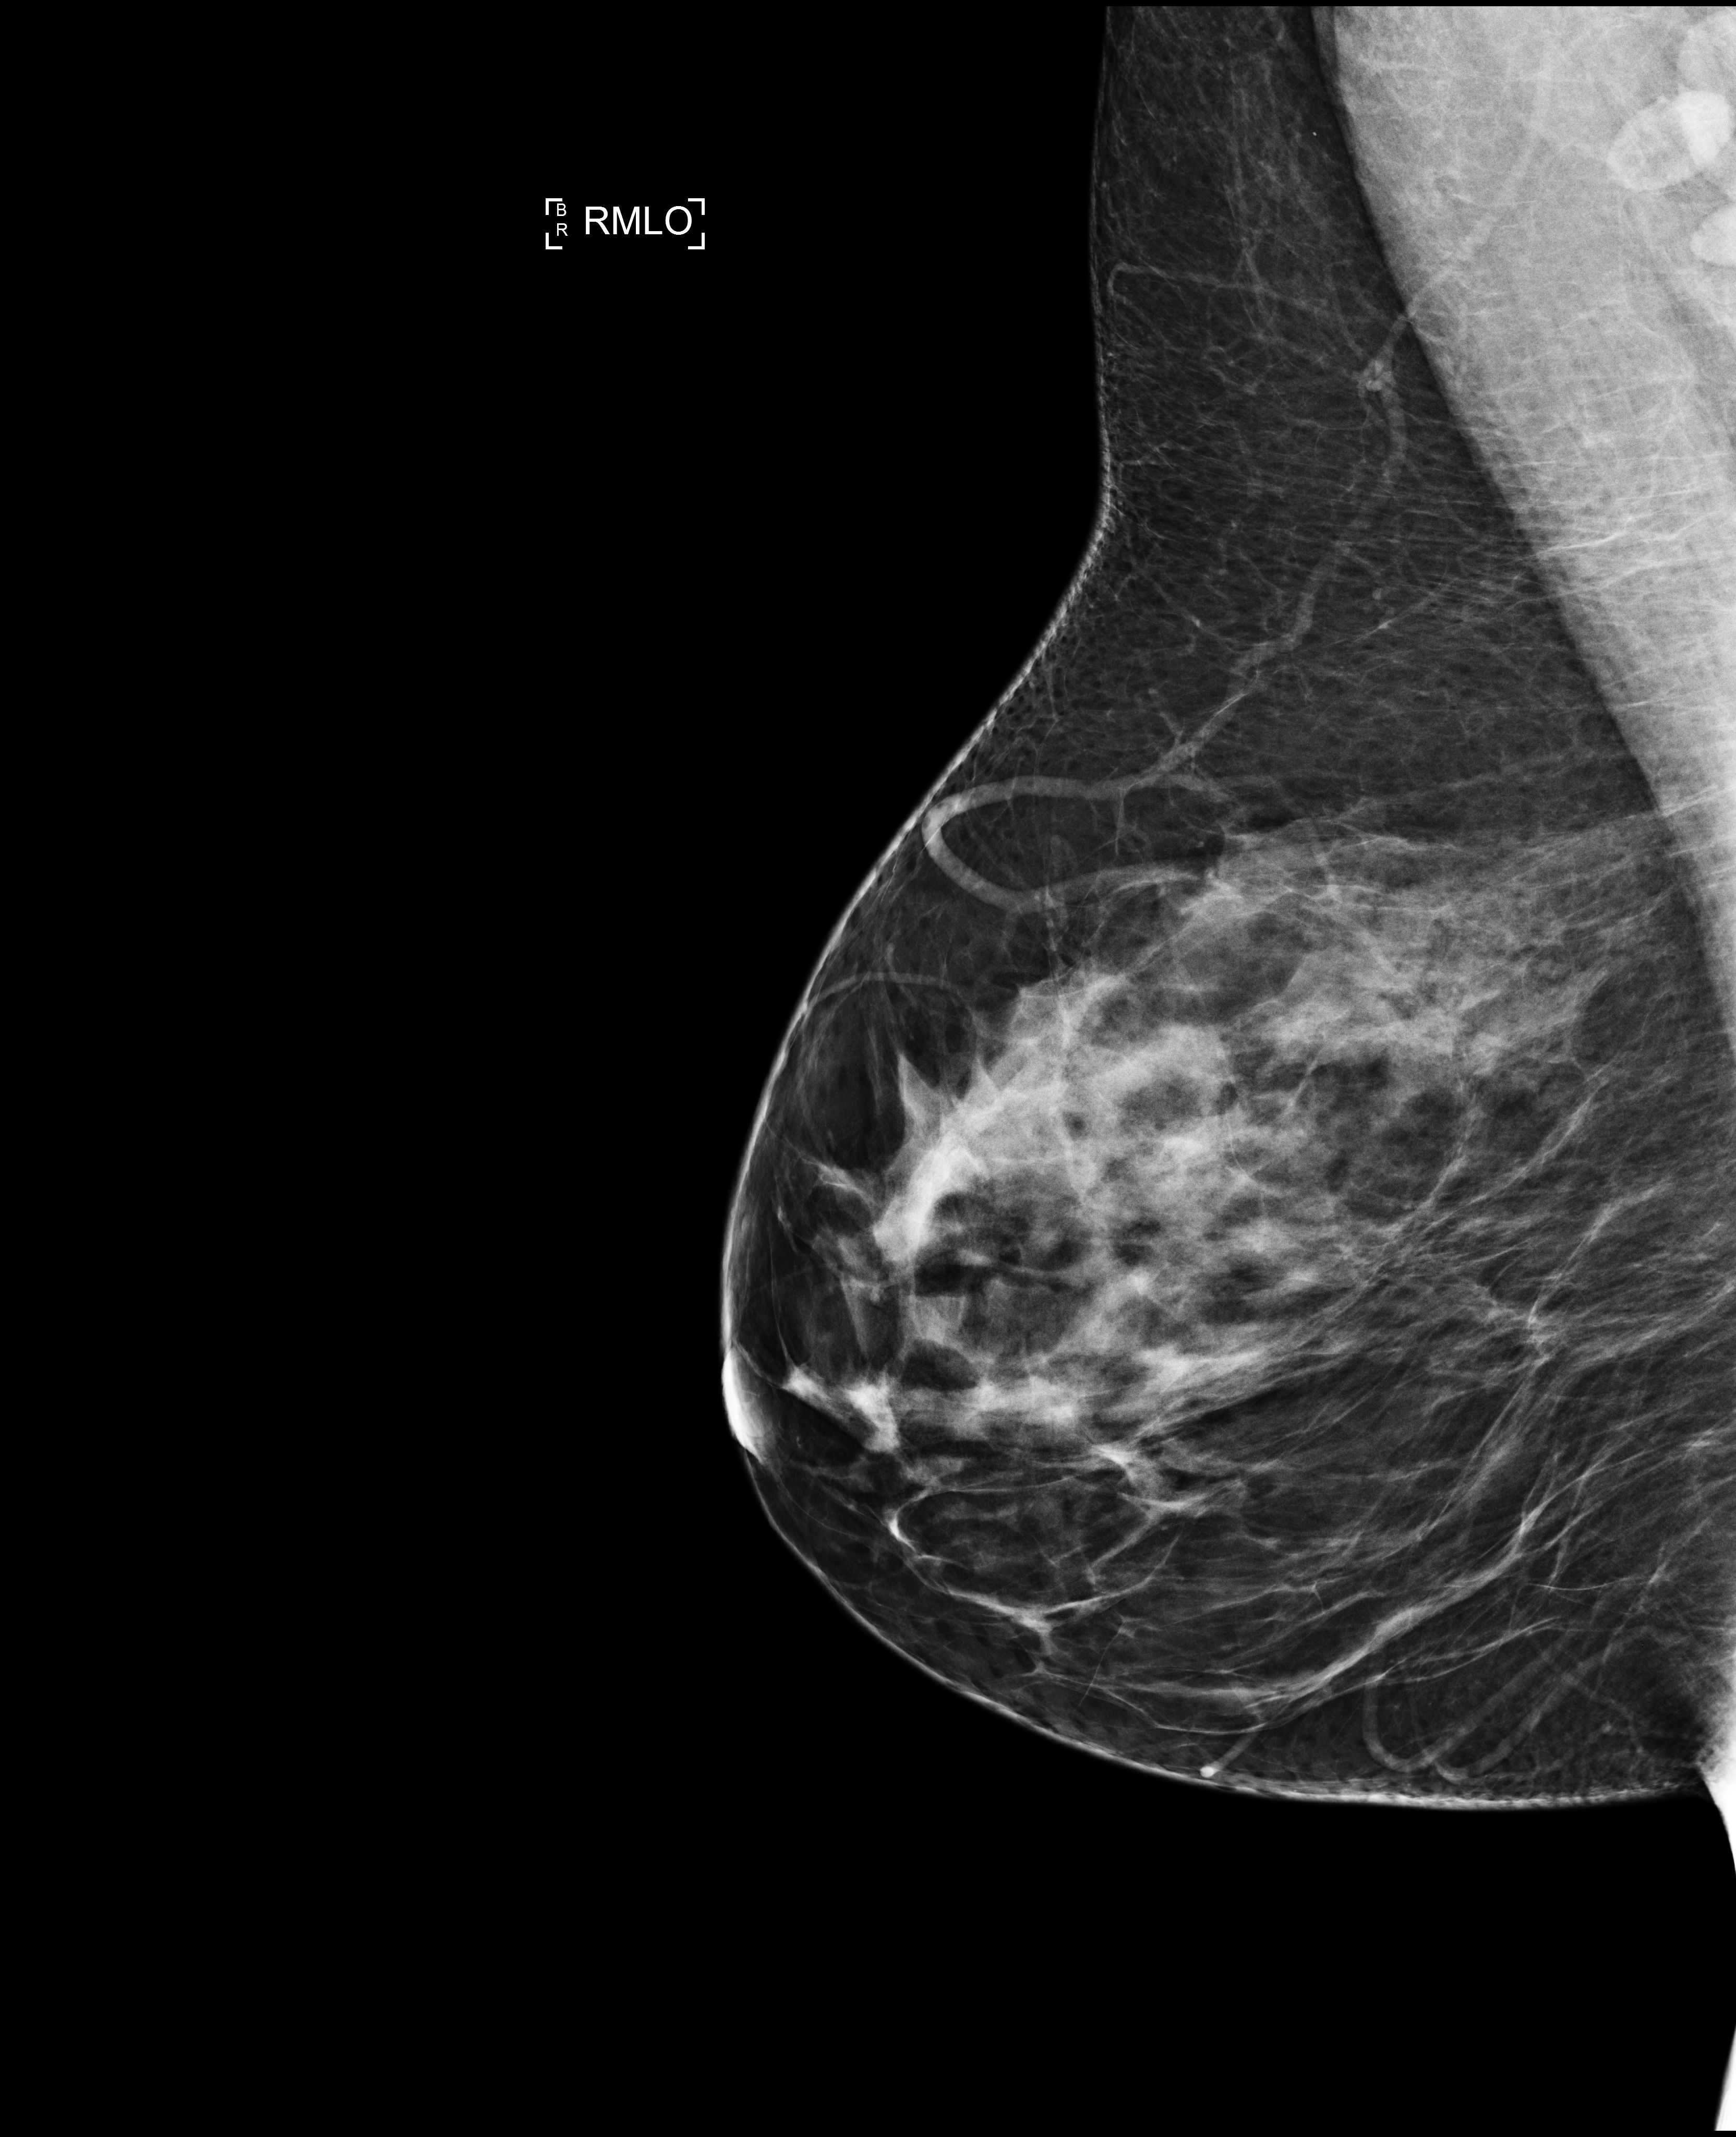
Annual screening mammography examination; compressed breast thickness 80 mm. Patient: female, 46 years.
Image type: full-field digital mammogram. Breast: right. Projection: MLO view.